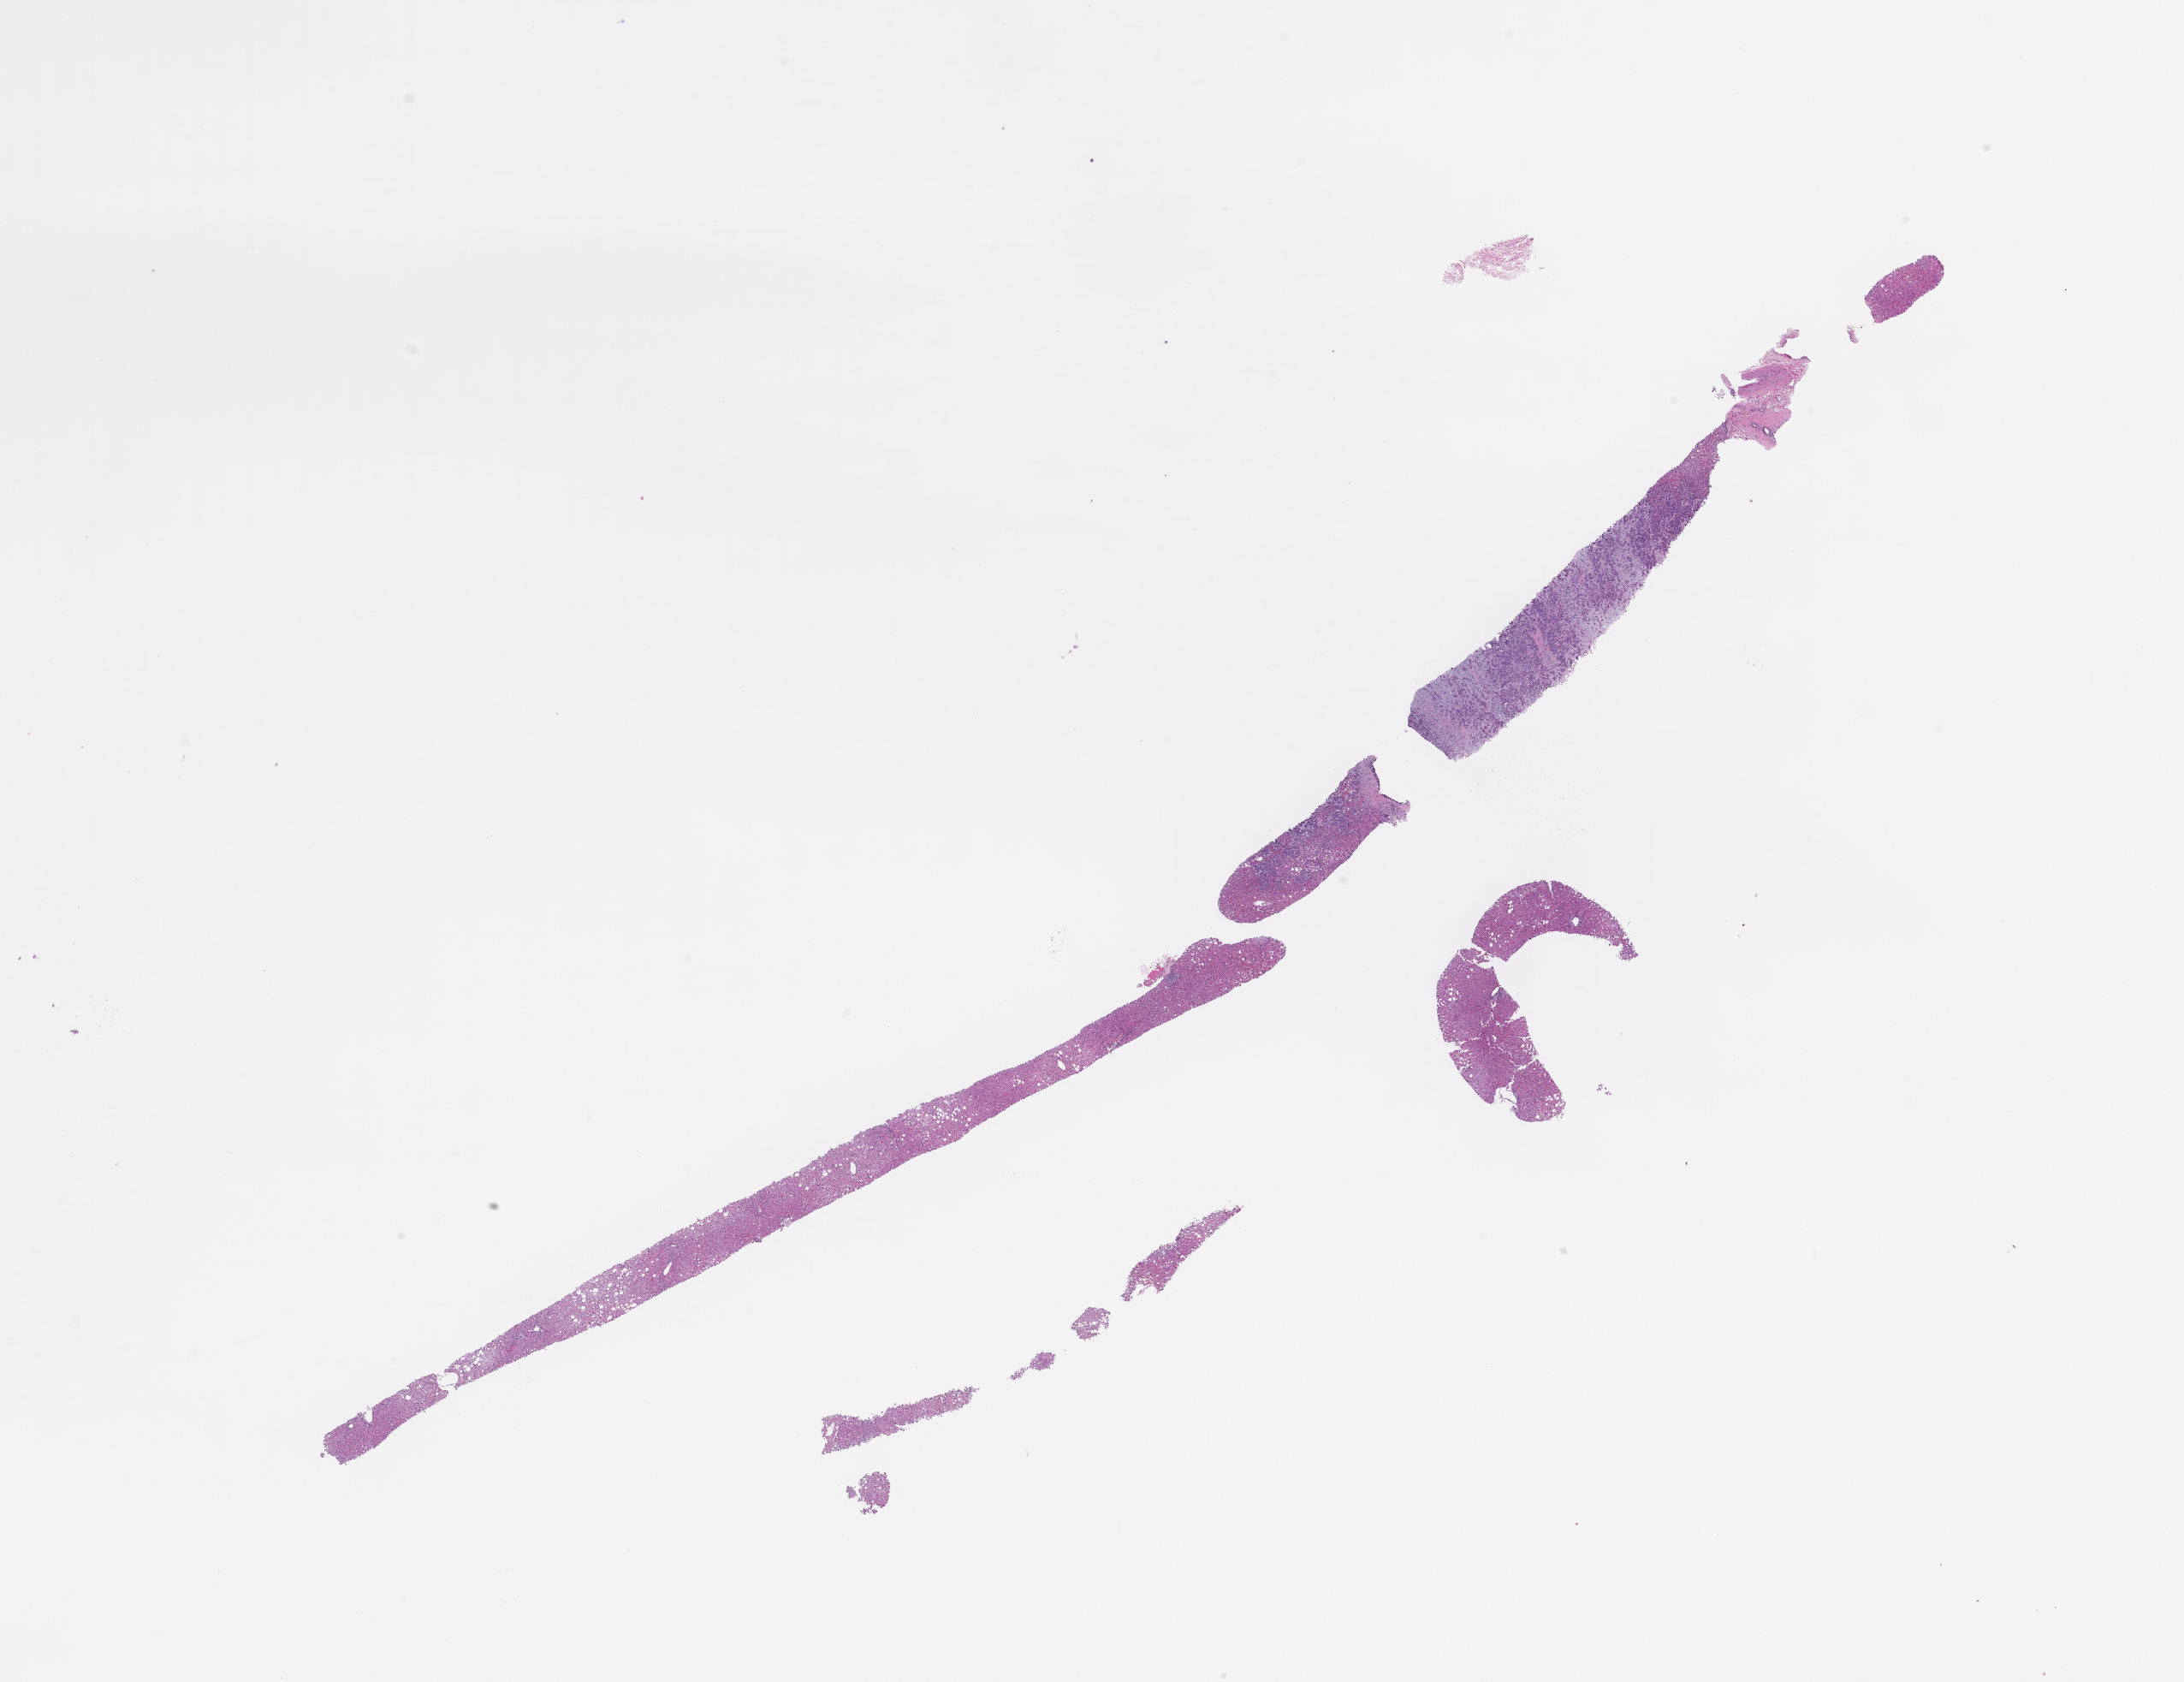
Digitized haematoxylin and eosin-stained section — a low-resolution overview of the entire scanned area, about 20.6 x 15.9 mm; formalin-fixed paraffin-embedded section. Female patient.
• this section: metastatic tumor tissue
• primary diagnosis of the patient: Invasive Breast Carcinoma